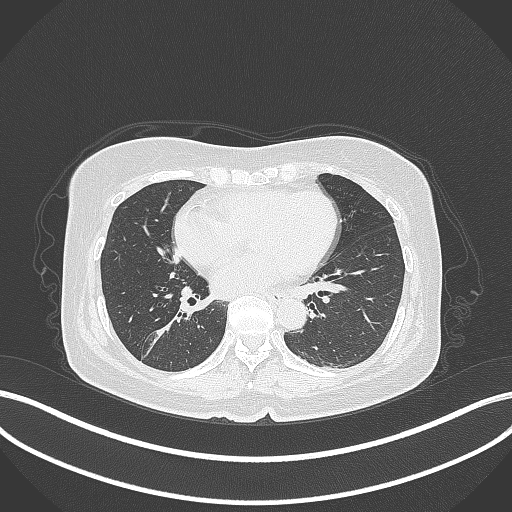
Chest CT, one axial slice; slice 173 of 429 in the series (ordered by position); 120 kVp; lung window (W 1500 / L -600 HU); 512 × 512 image matrix. Patient: female, 67 years. Case-level facts recorded for this patient, not image findings: clinical TNM (as recorded): T1c N1 M0; histopathological grade: G2-3.
Annotated regions visible in this slice (rectangle marked by the reading radiologist):
- lung tumour (recorded histology: adenocarcinoma): bounding box <154,304,199,349> (left, top, right, bottom; pixels)